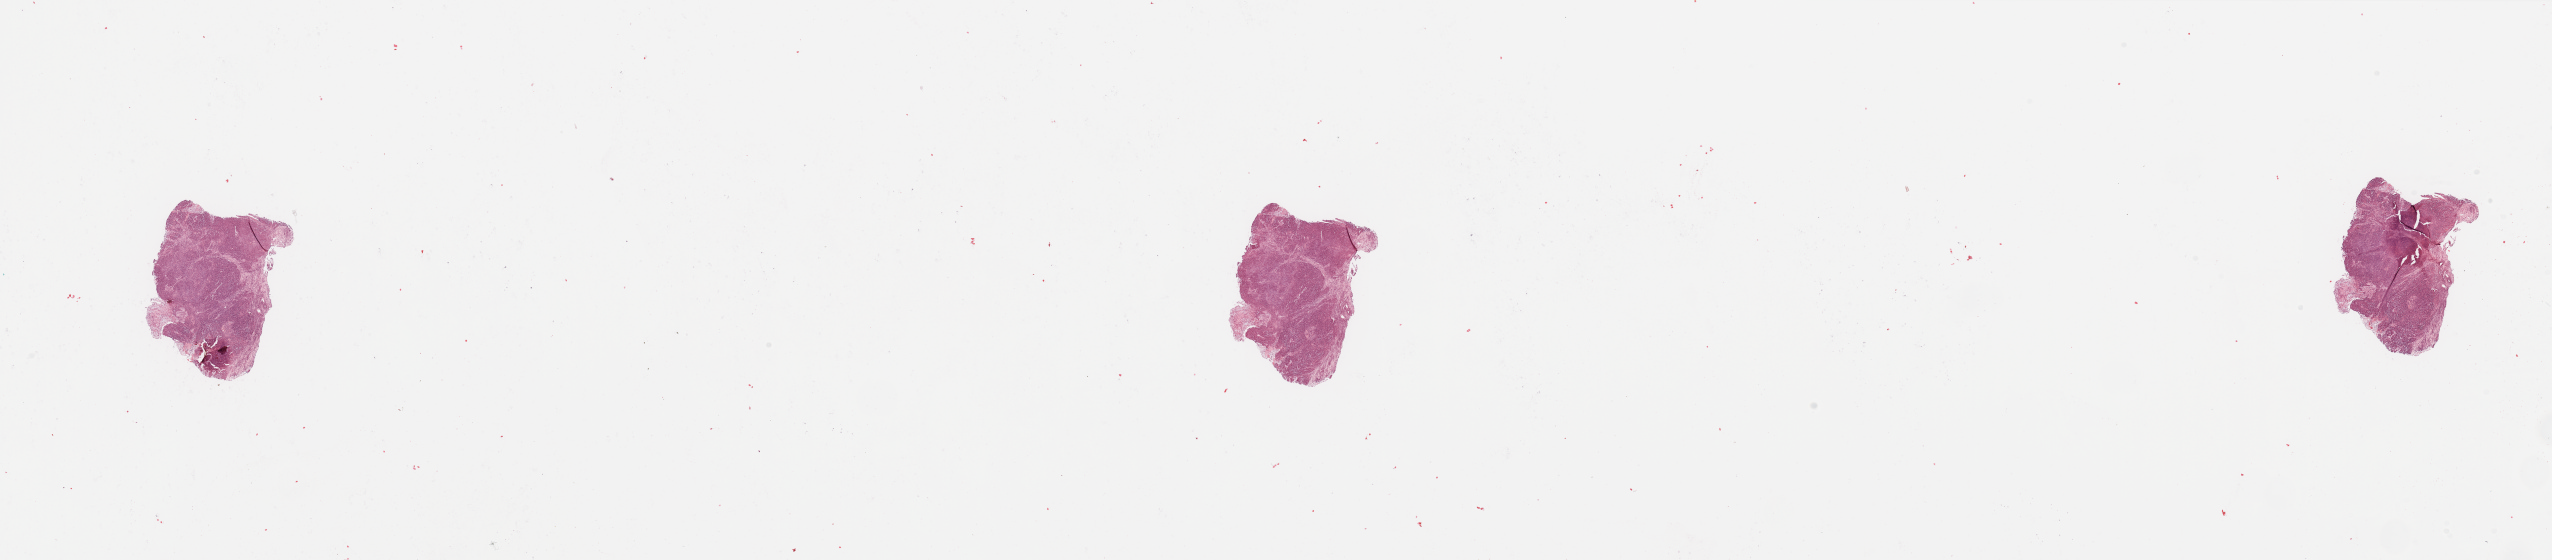
H&E-stained whole-slide image — shown as a low-resolution overview of the whole scanned area (about 40.4 x 8.9 mm). Tumour tissue sample, sampled site: larynx. Patient: male, age 62 years. Histologic grade: G3 (poorly differentiated). Composition of this section per pathologist review: tumour nuclei 90%, necrosis 0%.
• AJCC pathologic stage: IVA
• histologic diagnosis: Squamous cell carcinoma, NOS (larynx, NOS)
• primary tumour site (as recorded): larynx